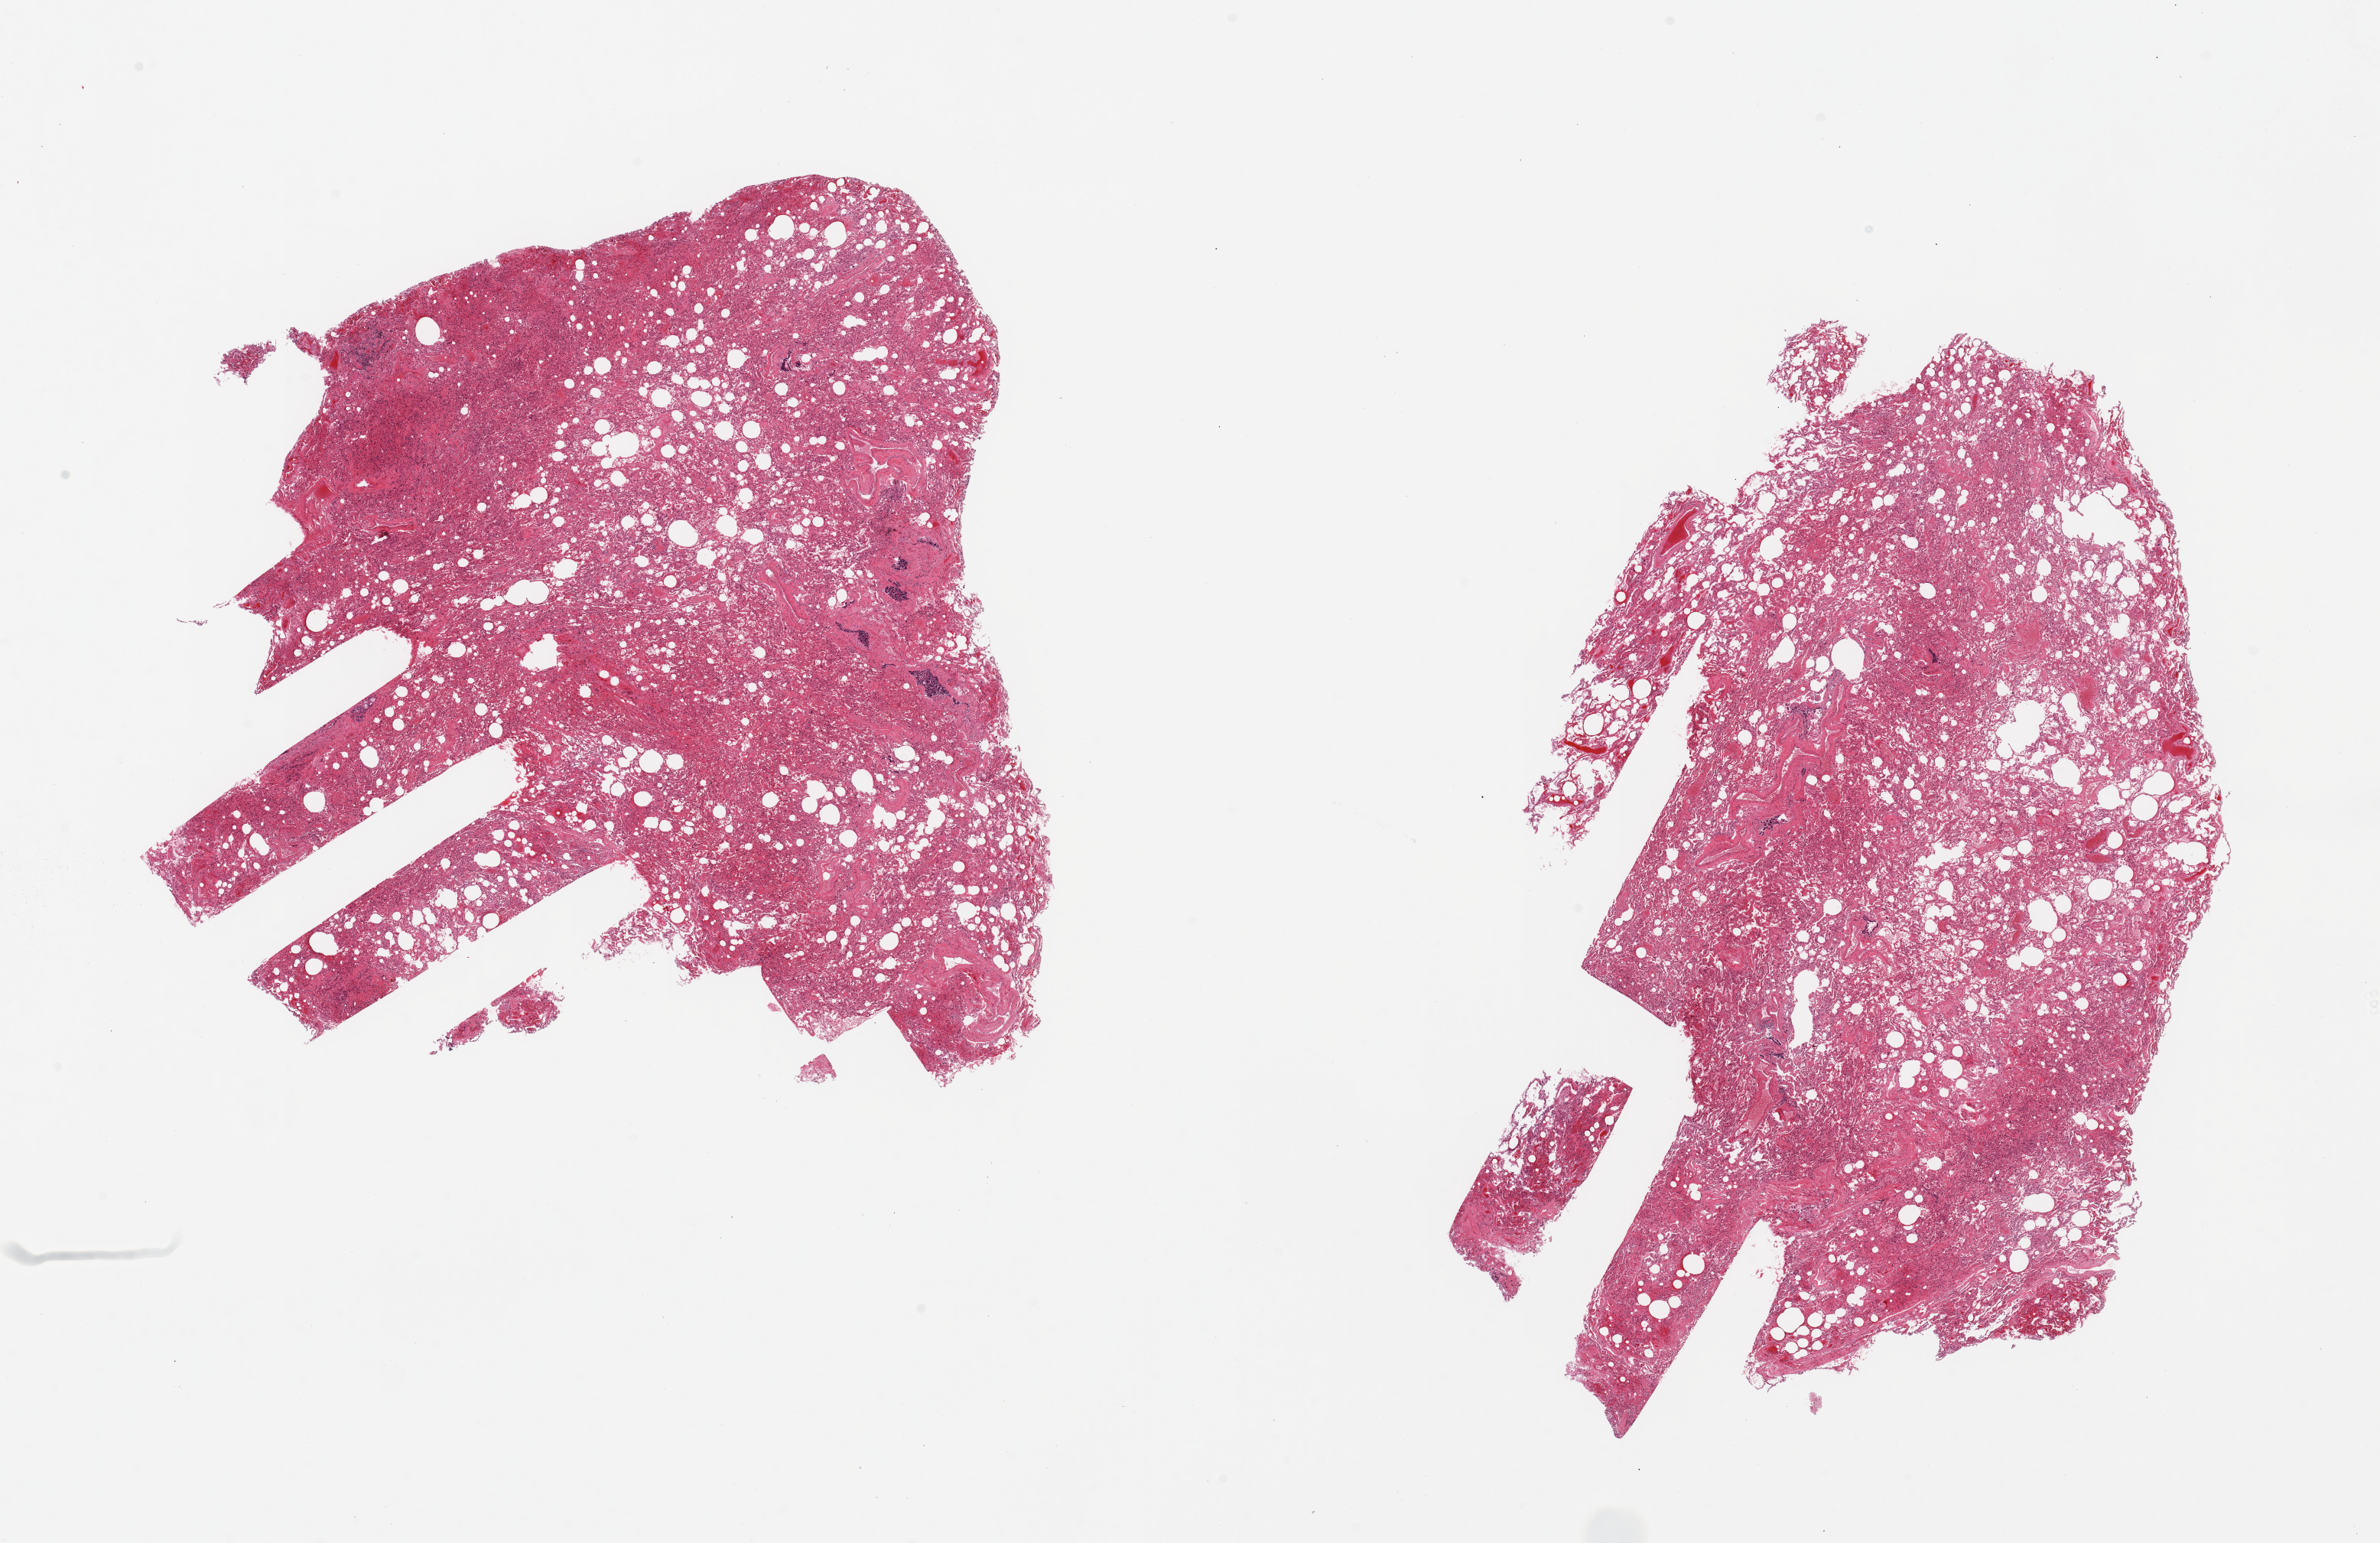
Whole-slide image, hematoxylin and eosin (H&E) stain, shown as a low-resolution overview of the whole scanned area (about 24.6 x 16.0 mm, acquisition: 20x scan), PAXgene-fixed, paraffin-embedded tissue, sampled site (target tissue): lung, donor tissue sample. Male donor.
• reviewer comment on this tissue sample: 2 pieces; congestion and atelectasis